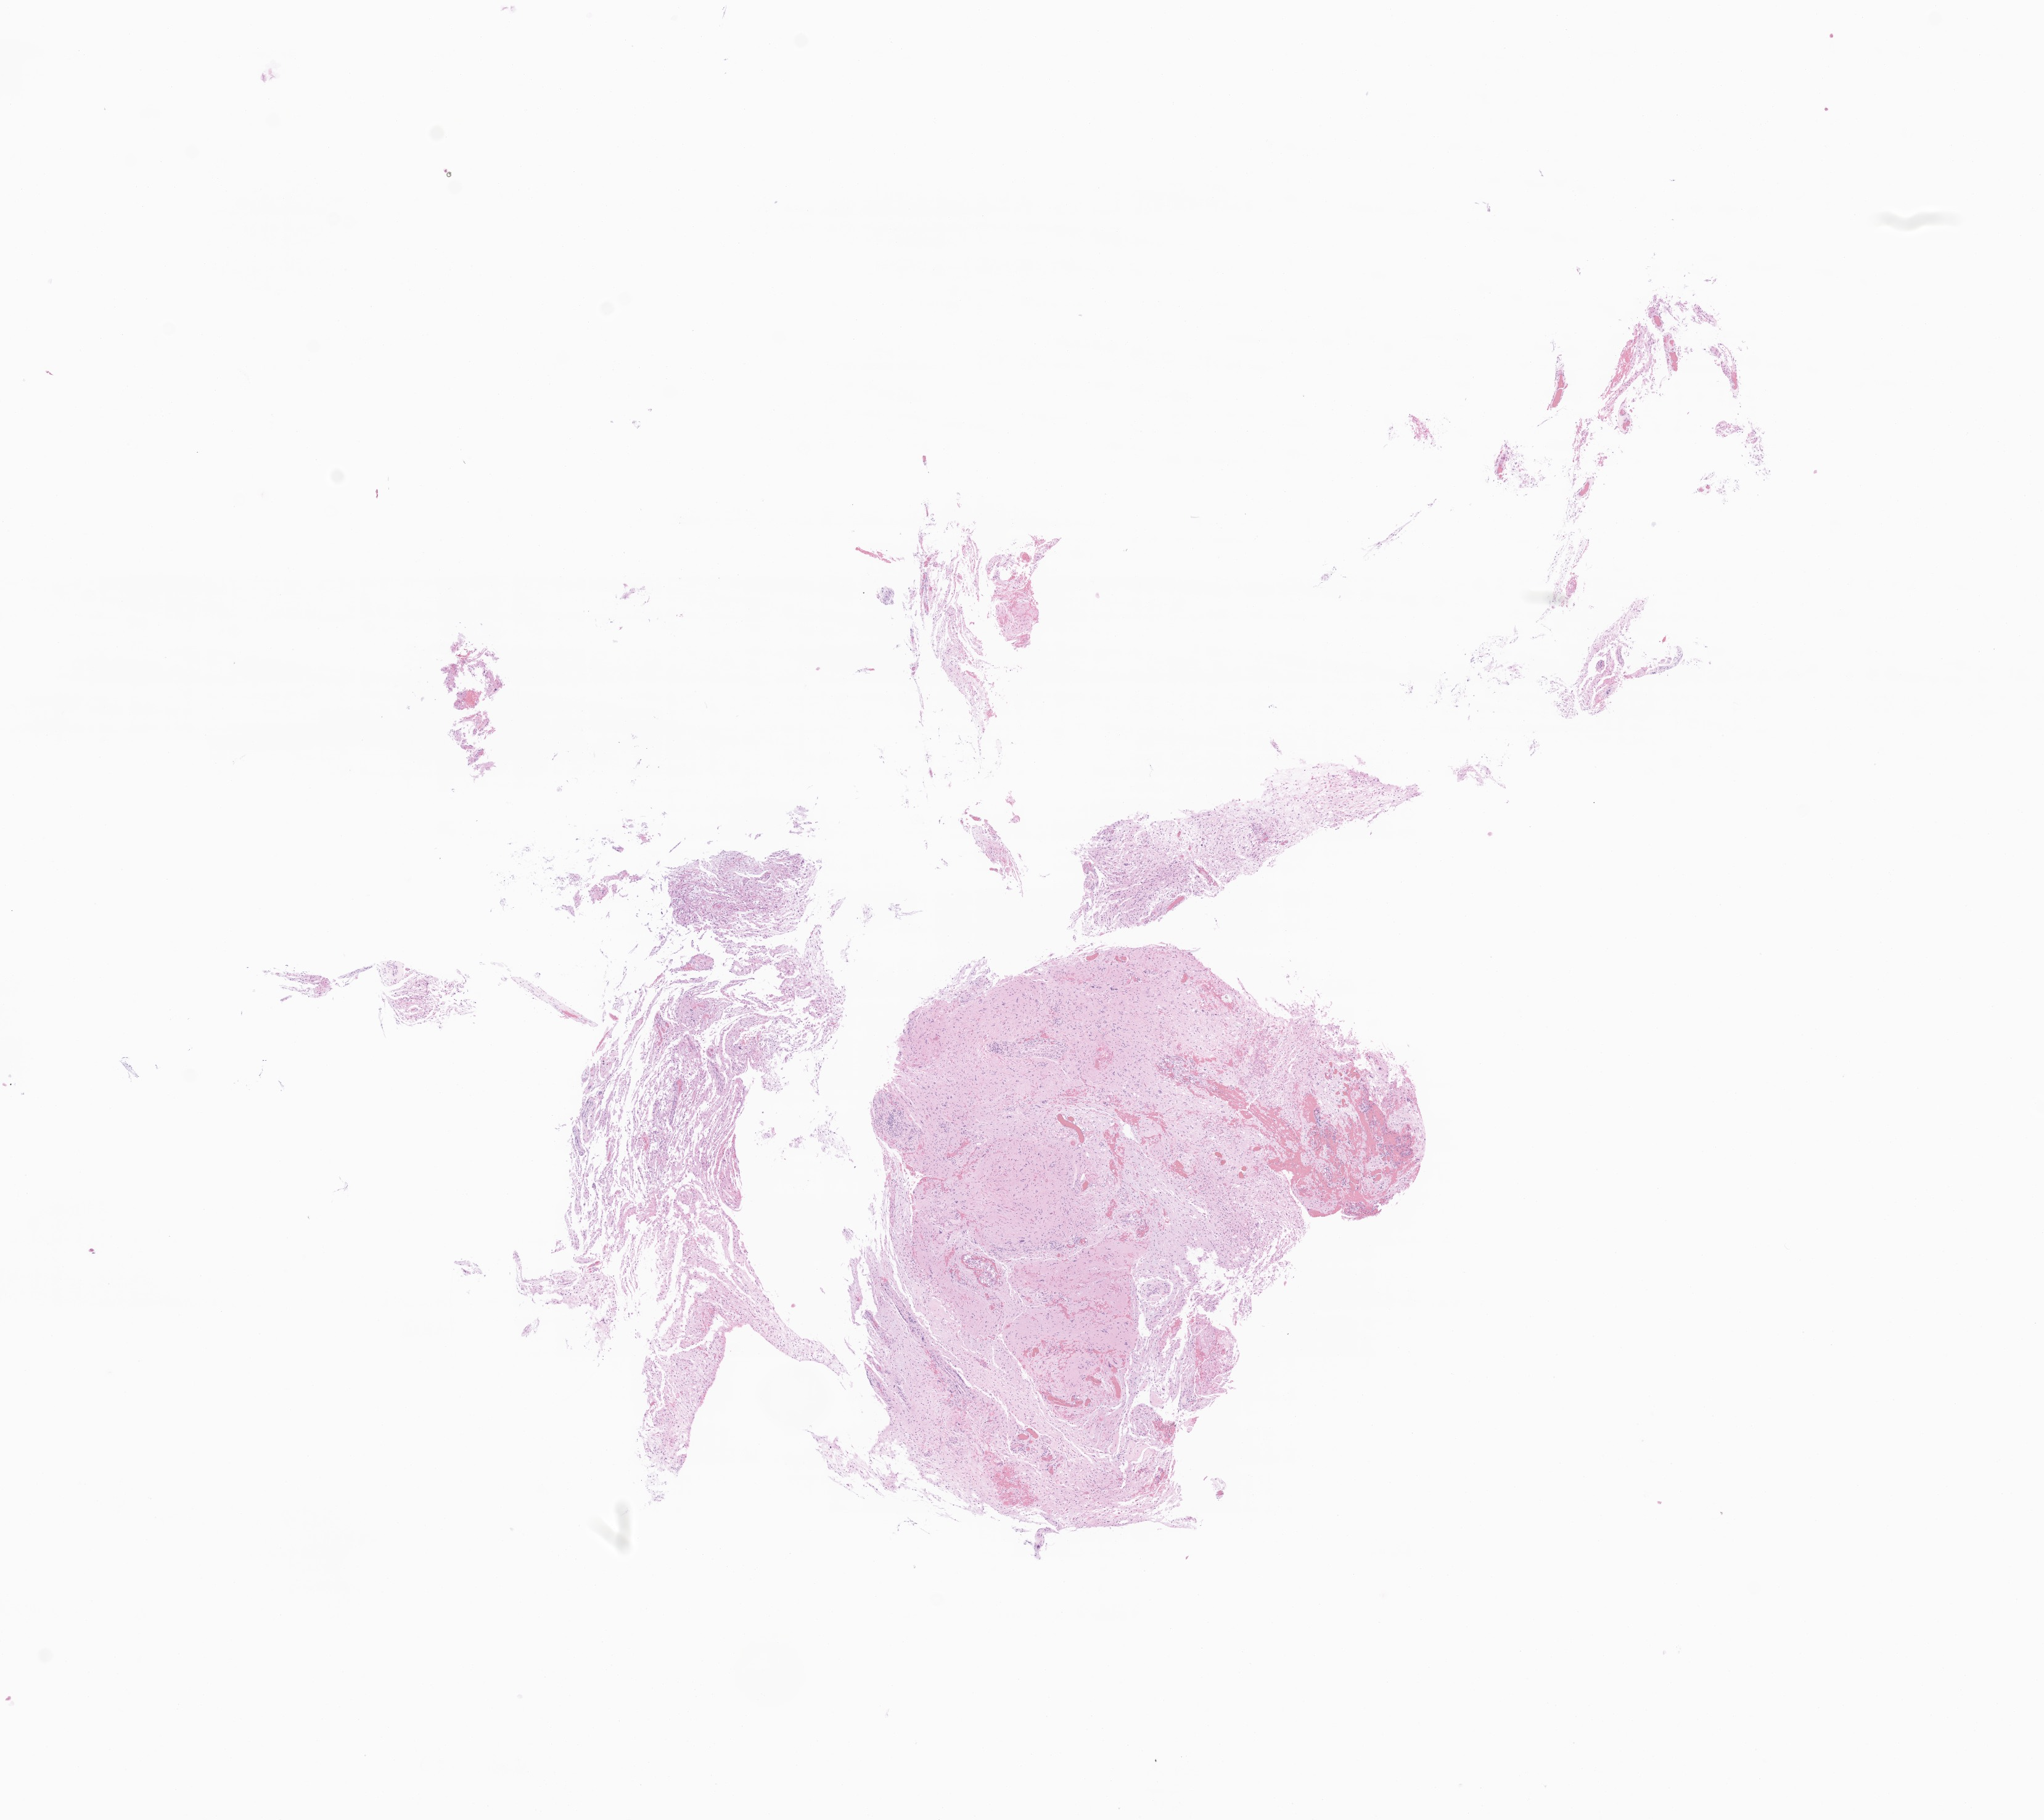
Digitized haematoxylin and eosin-stained section of tumor tissue from the cerebrum, low-resolution overview of the scanned area, about 14.0 x 12.4 mm; formalin-fixed, paraffin-embedded (FFPE) tissue. Patient female; age 170 months (14 years 2 months).
Diagnosis (ICD-O-3 morphology term): Pilocytic astrocytoma.